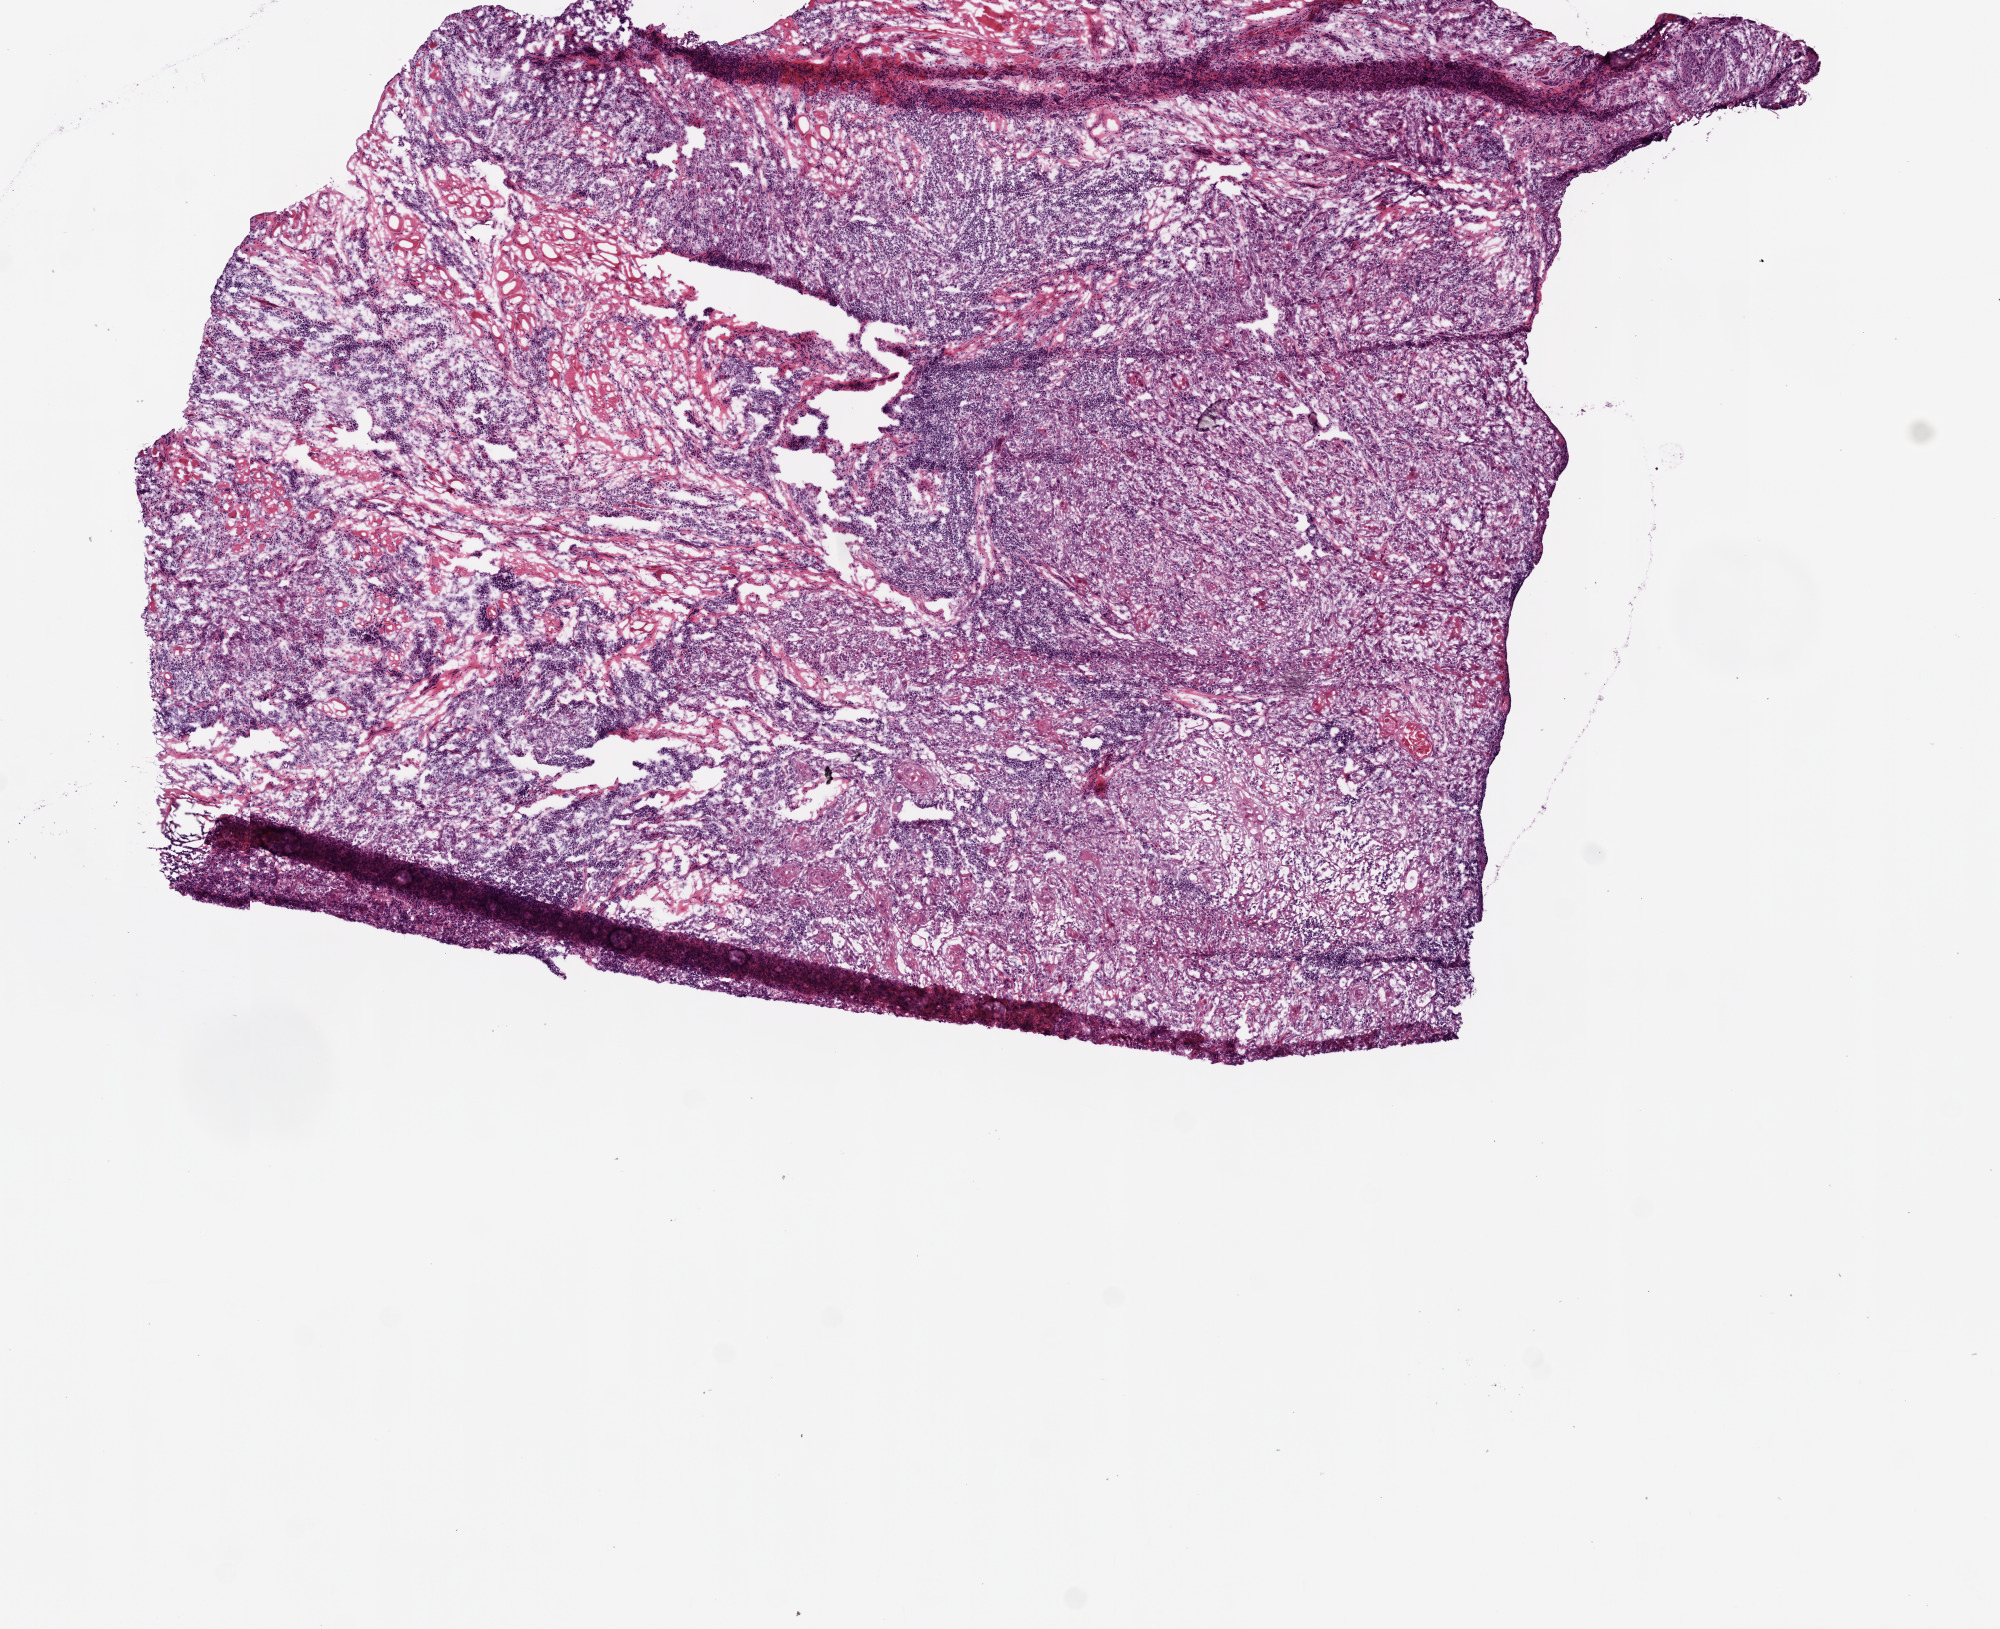
H&E-stained whole-slide image, low-resolution overview of the scanned area, about 8.0 x 6.5 mm. Frozen section. Primary tumour sample from the head and neck. Patient: male, age at initial diagnosis 61 years. Histologic grade: G3 (poorly differentiated). Slide review estimates, as recorded: tumour cells 85%, tumour nuclei 65%, normal cells 0%, stromal cells 15%, necrosis 0%.
* diagnosis: Squamous cell carcinoma, NOS (tongue, NOS)
* AJCC pathologic stage: III (7th edition)
* TNM: T1 N1